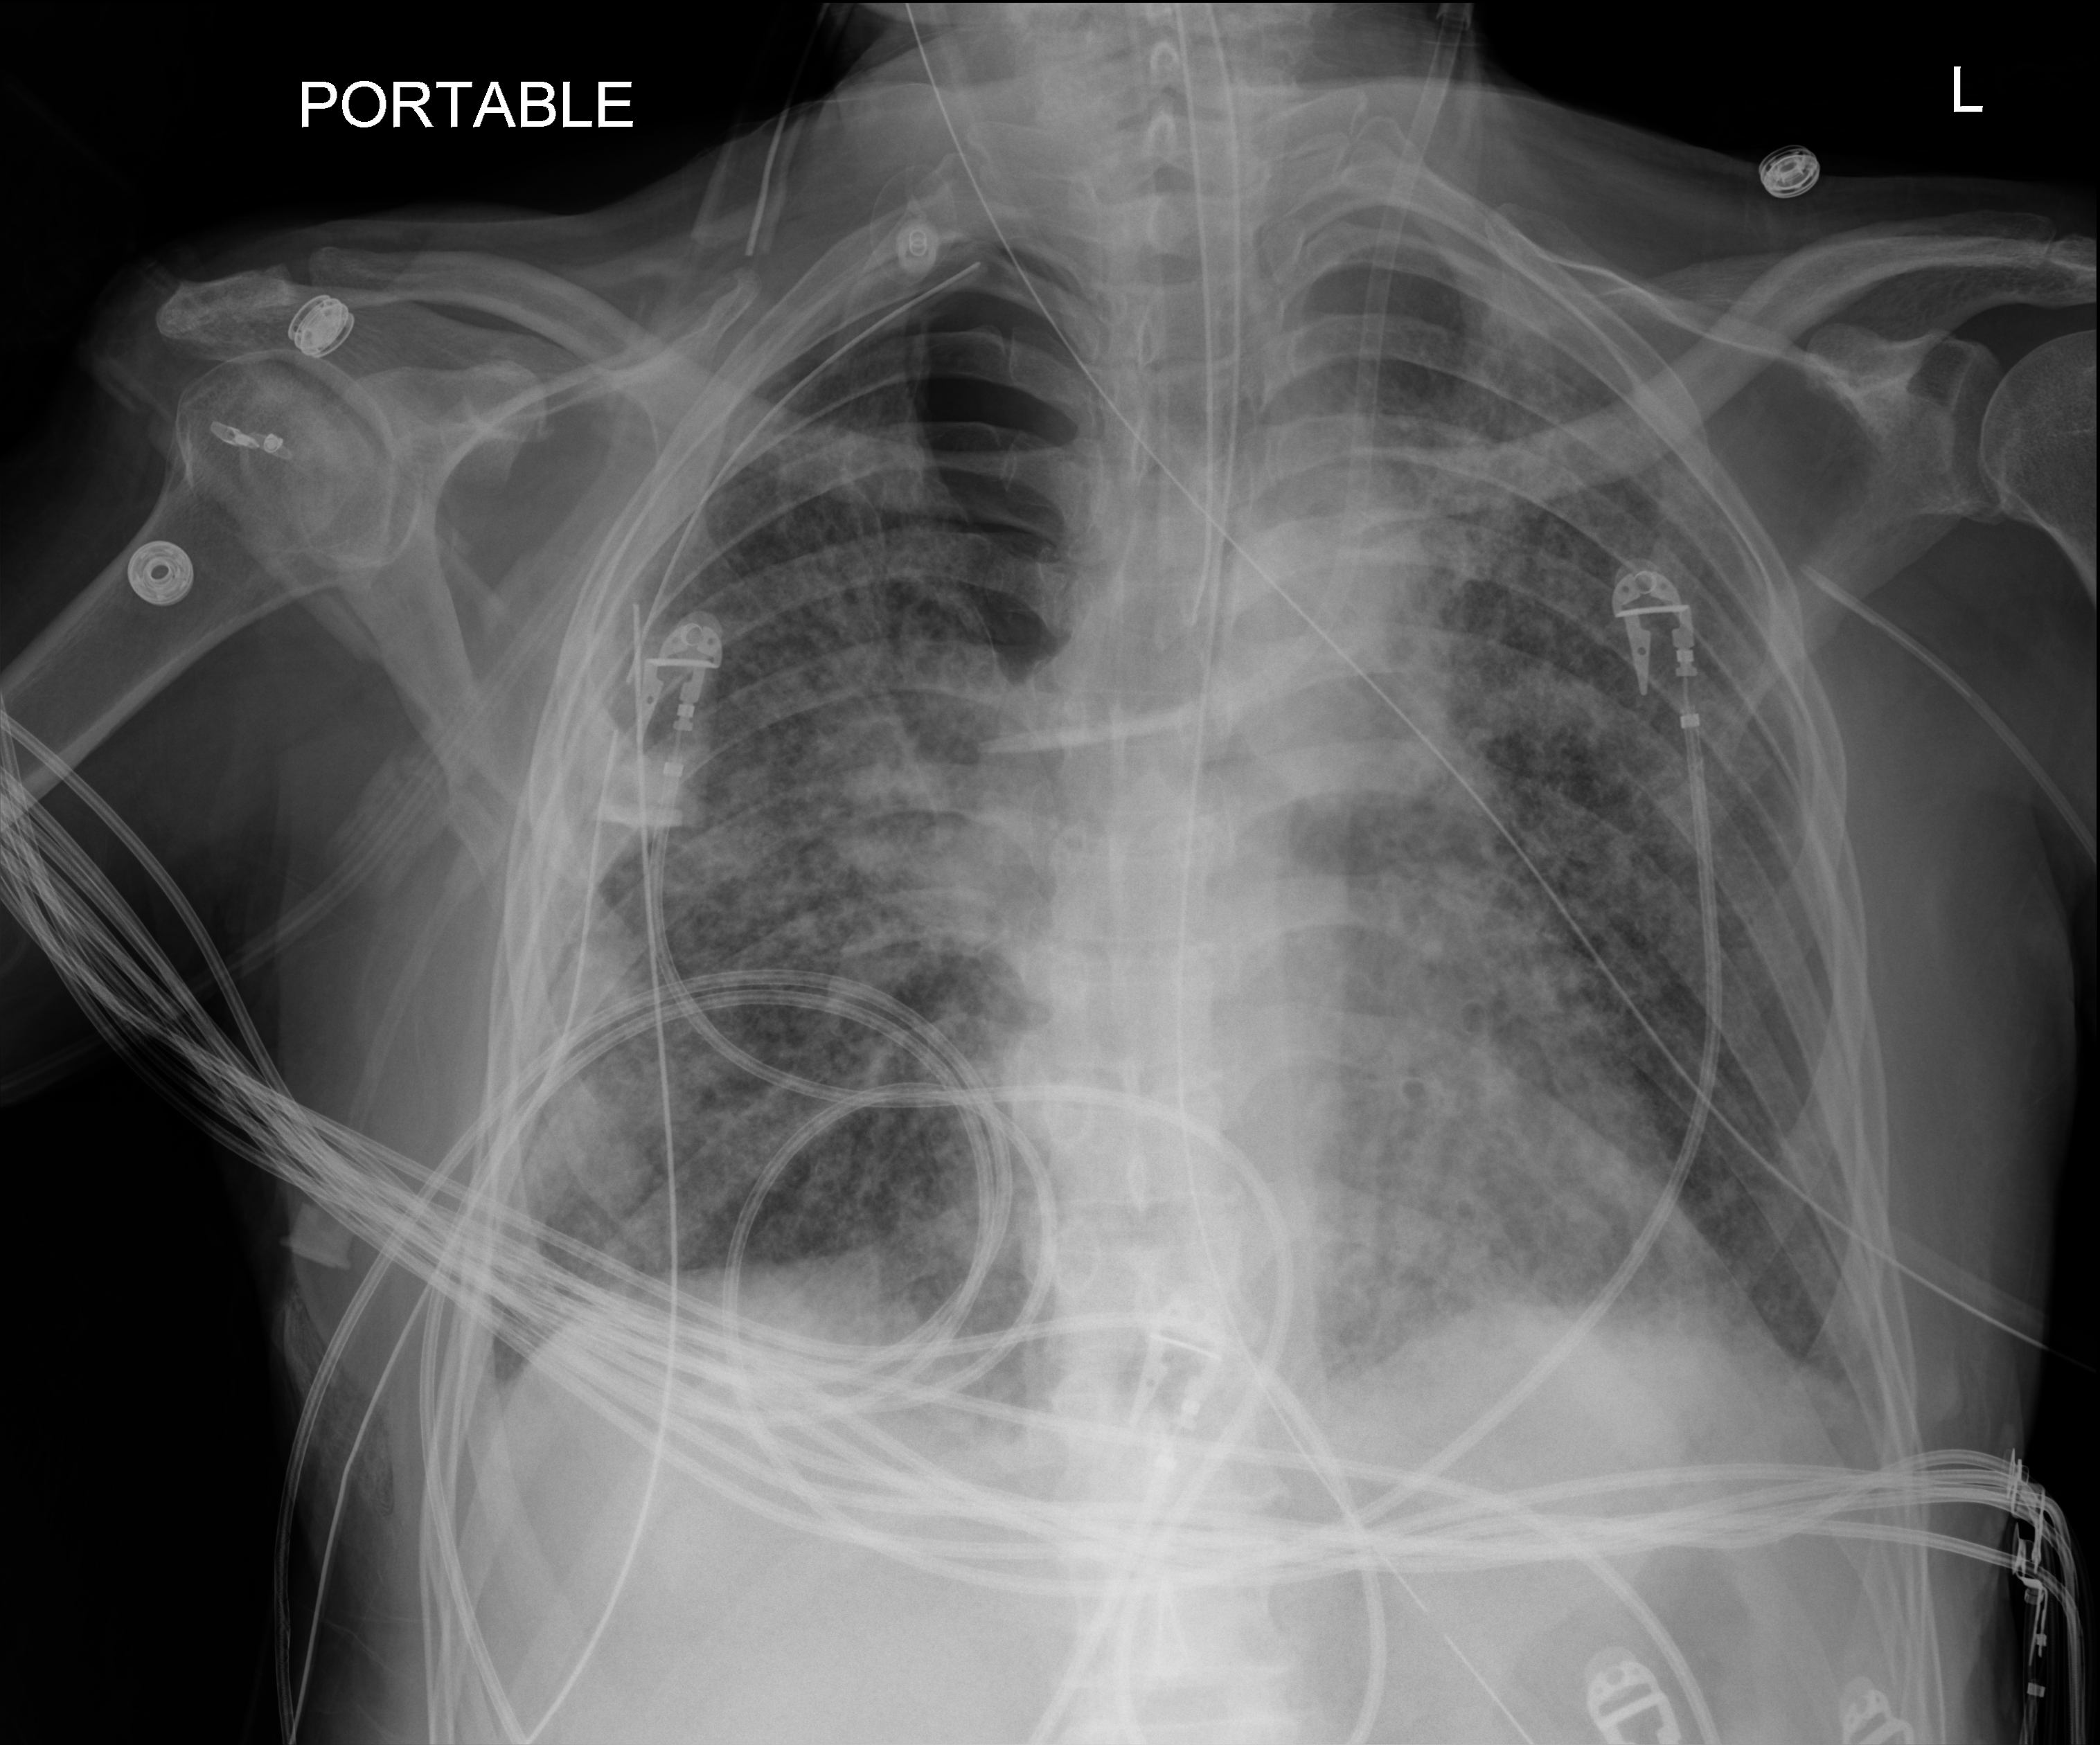
Chest radiograph, anteroposterior (AP) projection. Patient hospitalised with COVID-19; male, aged 60–74 years.
Admission-level facts for this patient (not findings on this image; timing relative to this image not recorded): mechanically ventilated during this hospital stay: yes; smoking status (admission record): never; admitted to intensive care during this hospital stay: yes.